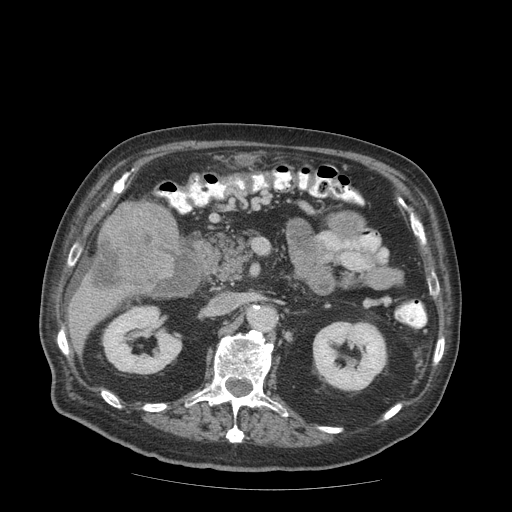
Contrast-enhanced abdominal CT (liver protocol), one axial slice; reconstruction kernel STANDARD; 140 kVp; soft-tissue window (W 400 / L 40 HU); 2.5 mm slice thickness; 512 × 512 image matrix. Case-level facts recorded for this patient, not image findings: diagnosis: hepatocellular carcinoma (patient treated with transarterial chemoembolisation; whether this scan precedes or follows treatment is not stated here); TNM stage (as recorded): Stage-IIIB; Child-Pugh class: A; tumour differentiation: well differentiated; tumour nodularity: multinodular.
Outlined on this slice (semi-automatically segmented with operator editing):
- liver parenchyma outside the tumour (the mass and vessels are separate outlines, so this box may not span the whole liver): box from (x=68, y=206) to (x=182, y=346) px
- mass: (x=87, y=198)–(x=178, y=292)